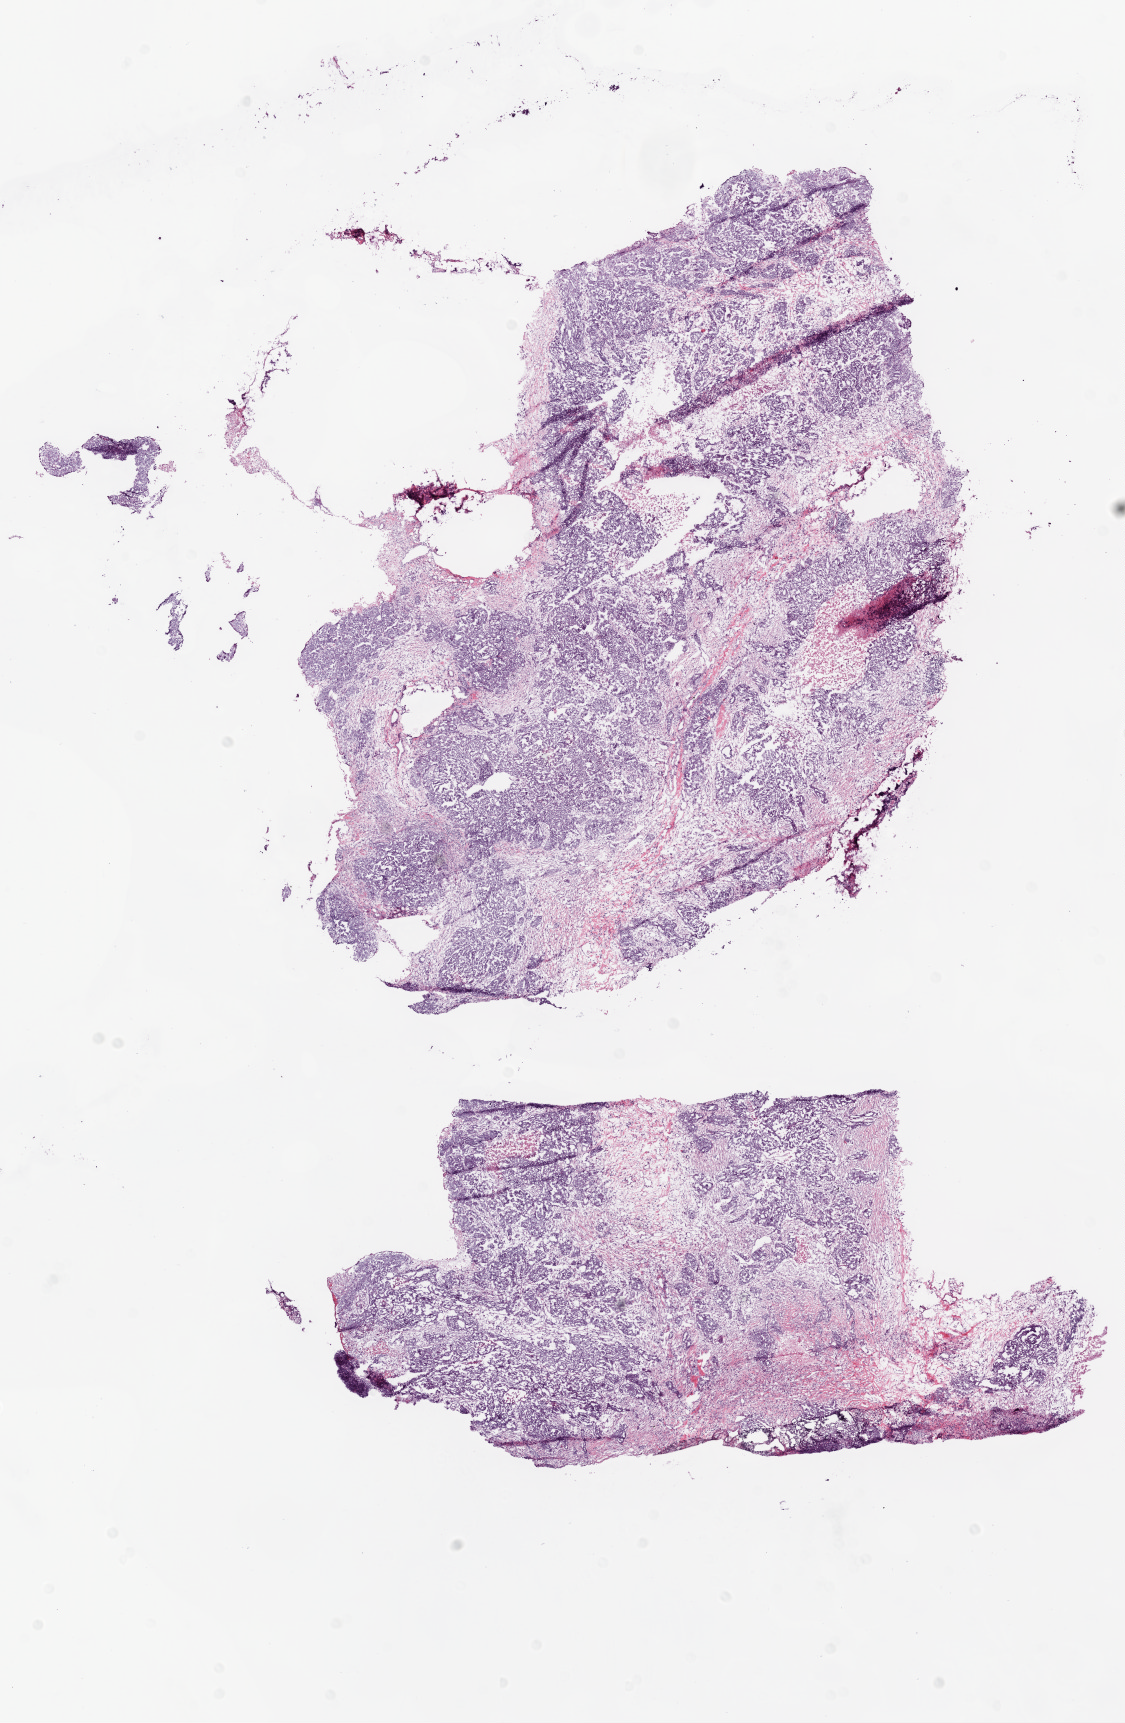
Digitized Hematoxylin and eosin (H&E) stained tissue section (whole slide), low-resolution overview of the scanned area, about 9.0 x 13.8 mm, frozen section from the bottom of the tissue portion, sample: primary tumour, ovary. Patient: female, age at initial diagnosis 65 years. Histologic grade: G2 (moderately differentiated). Composition of this section per pathologist review: tumour cells 70%, tumour nuclei 80%, normal cells 0%, stromal cells 30%, necrosis 0%.
- FIGO stage: IV
- pathologic diagnosis: Serous cystadenocarcinoma, NOS